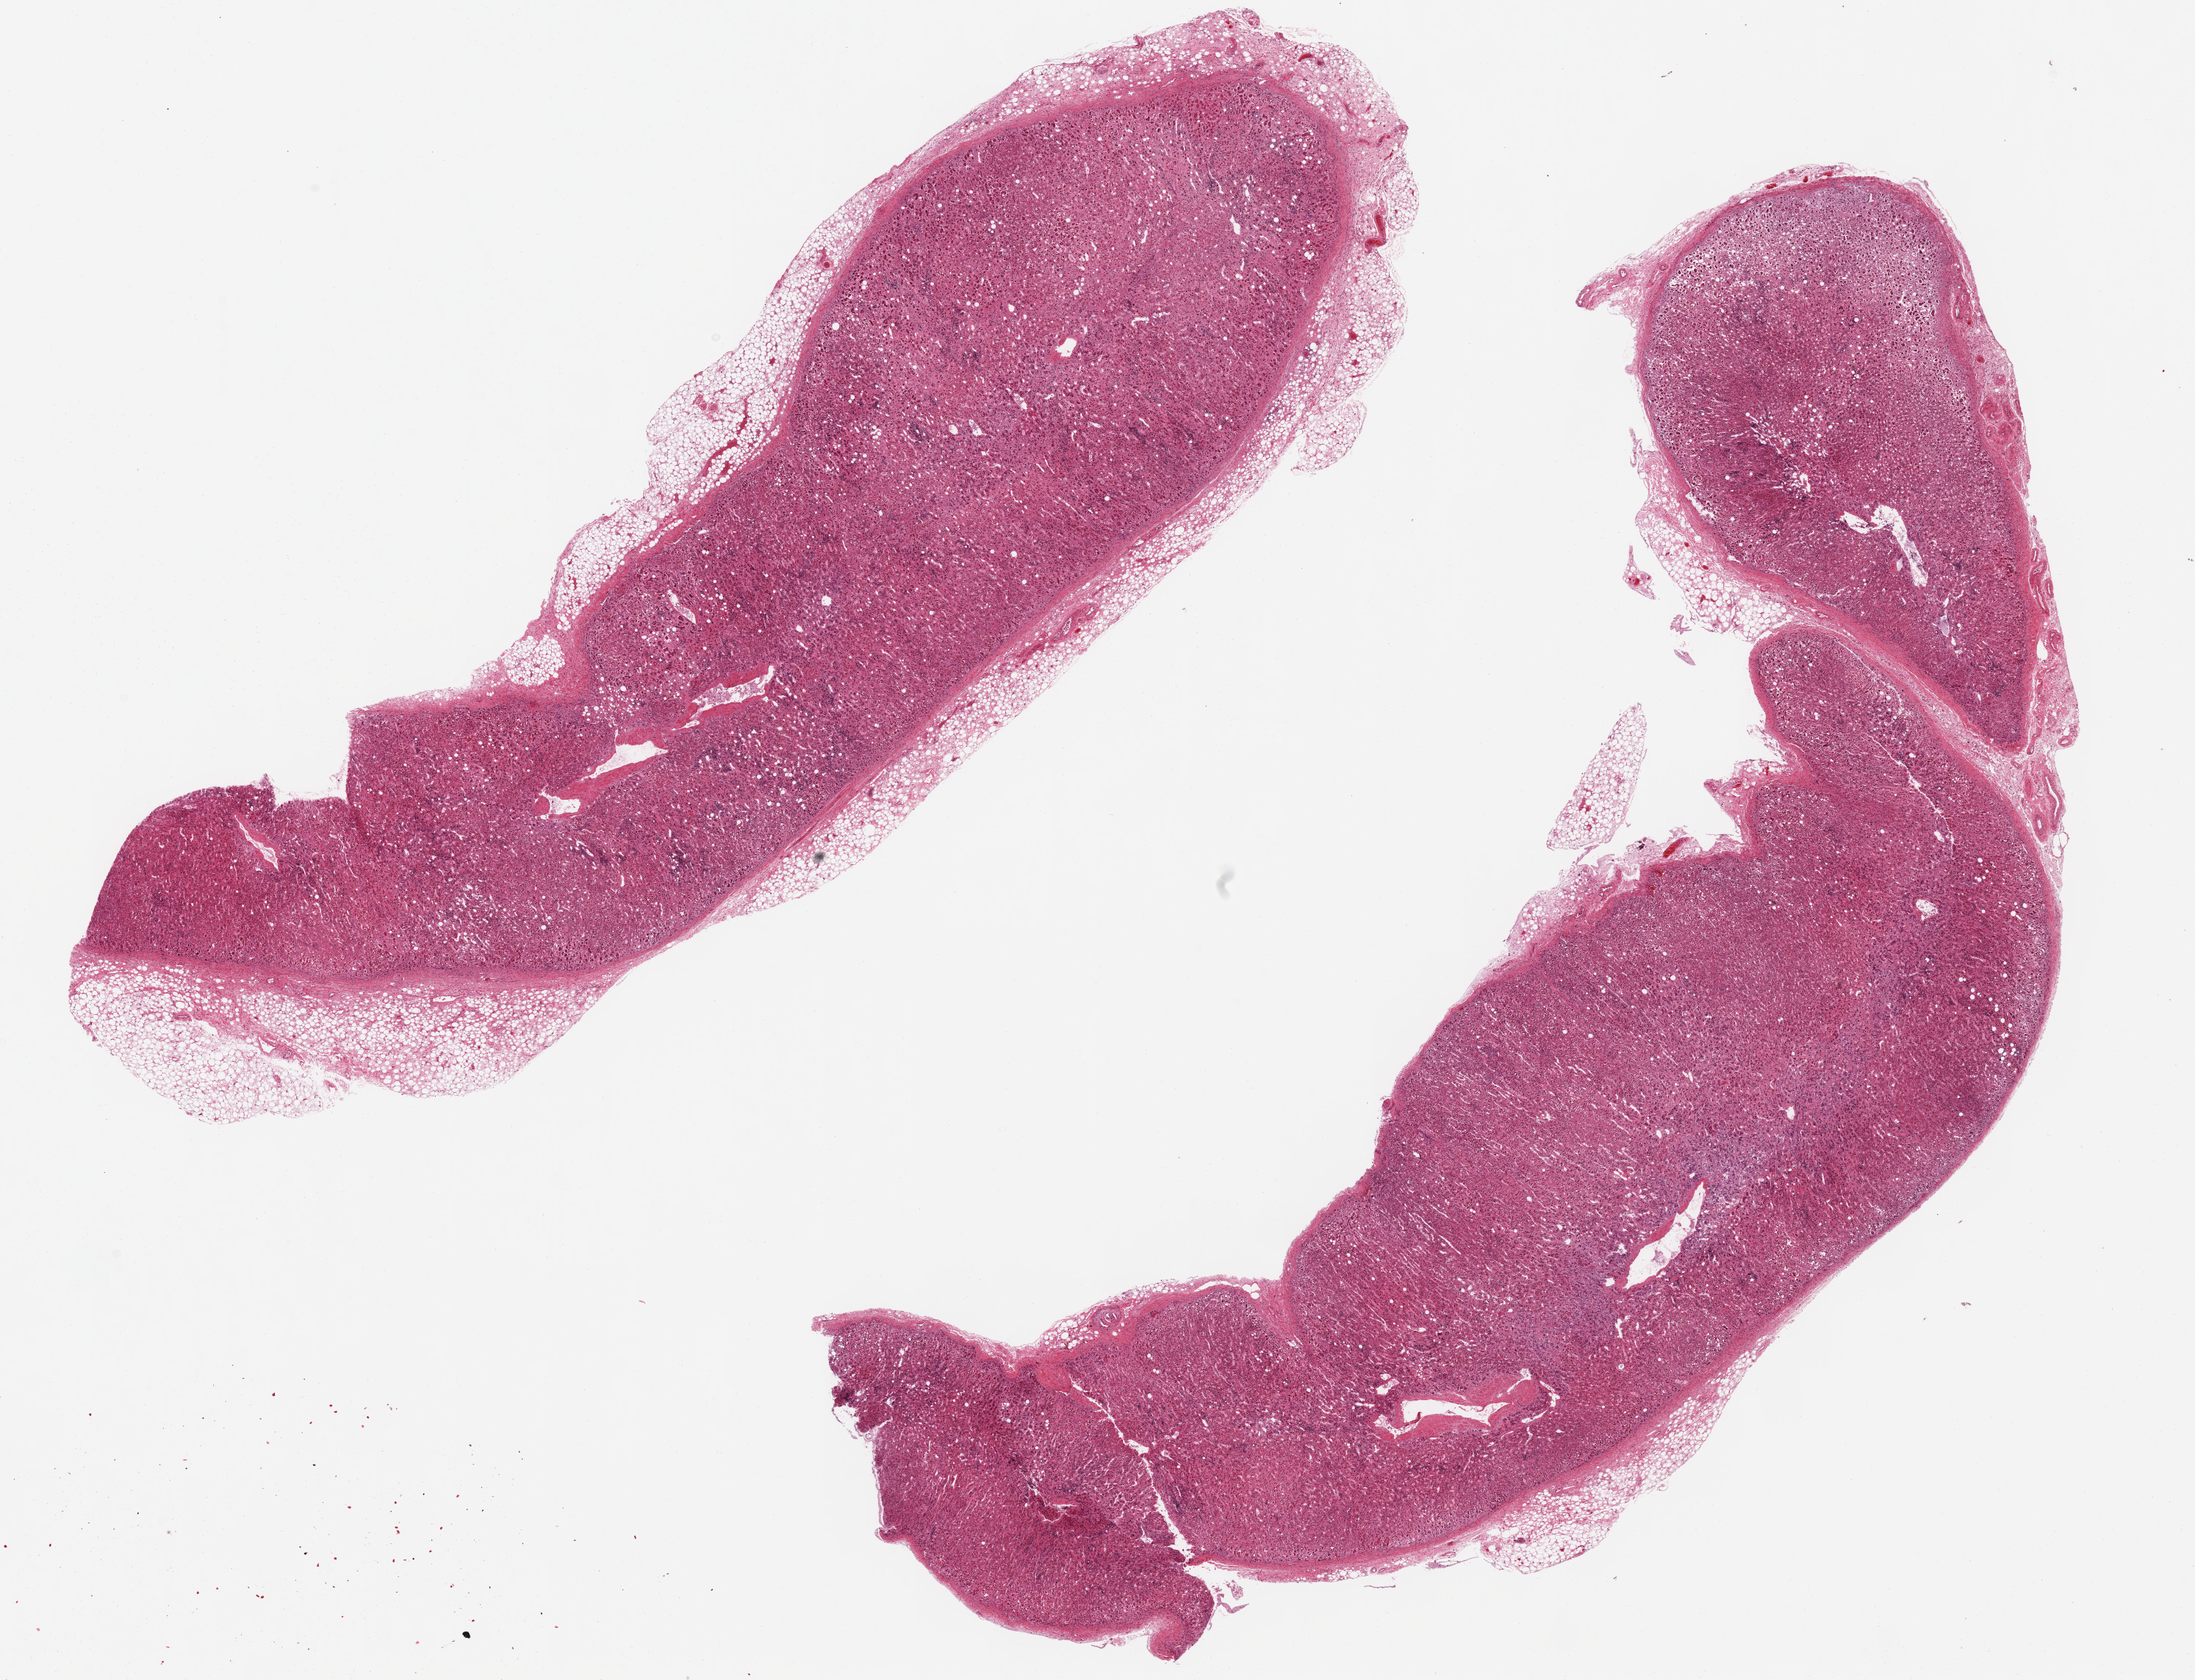
H&E whole-slide image — a low-resolution overview of the entire scanned area, about 23.6 x 18.1 mm; PAXgene-fixed paraffin-embedded (PFPE) section; target tissue: adrenal gland; donor tissue sample. Donor: female.
Reviewer comment on this tissue sample: 2 ~ 15x5mm aliquots, minute amounts of adherent fat.